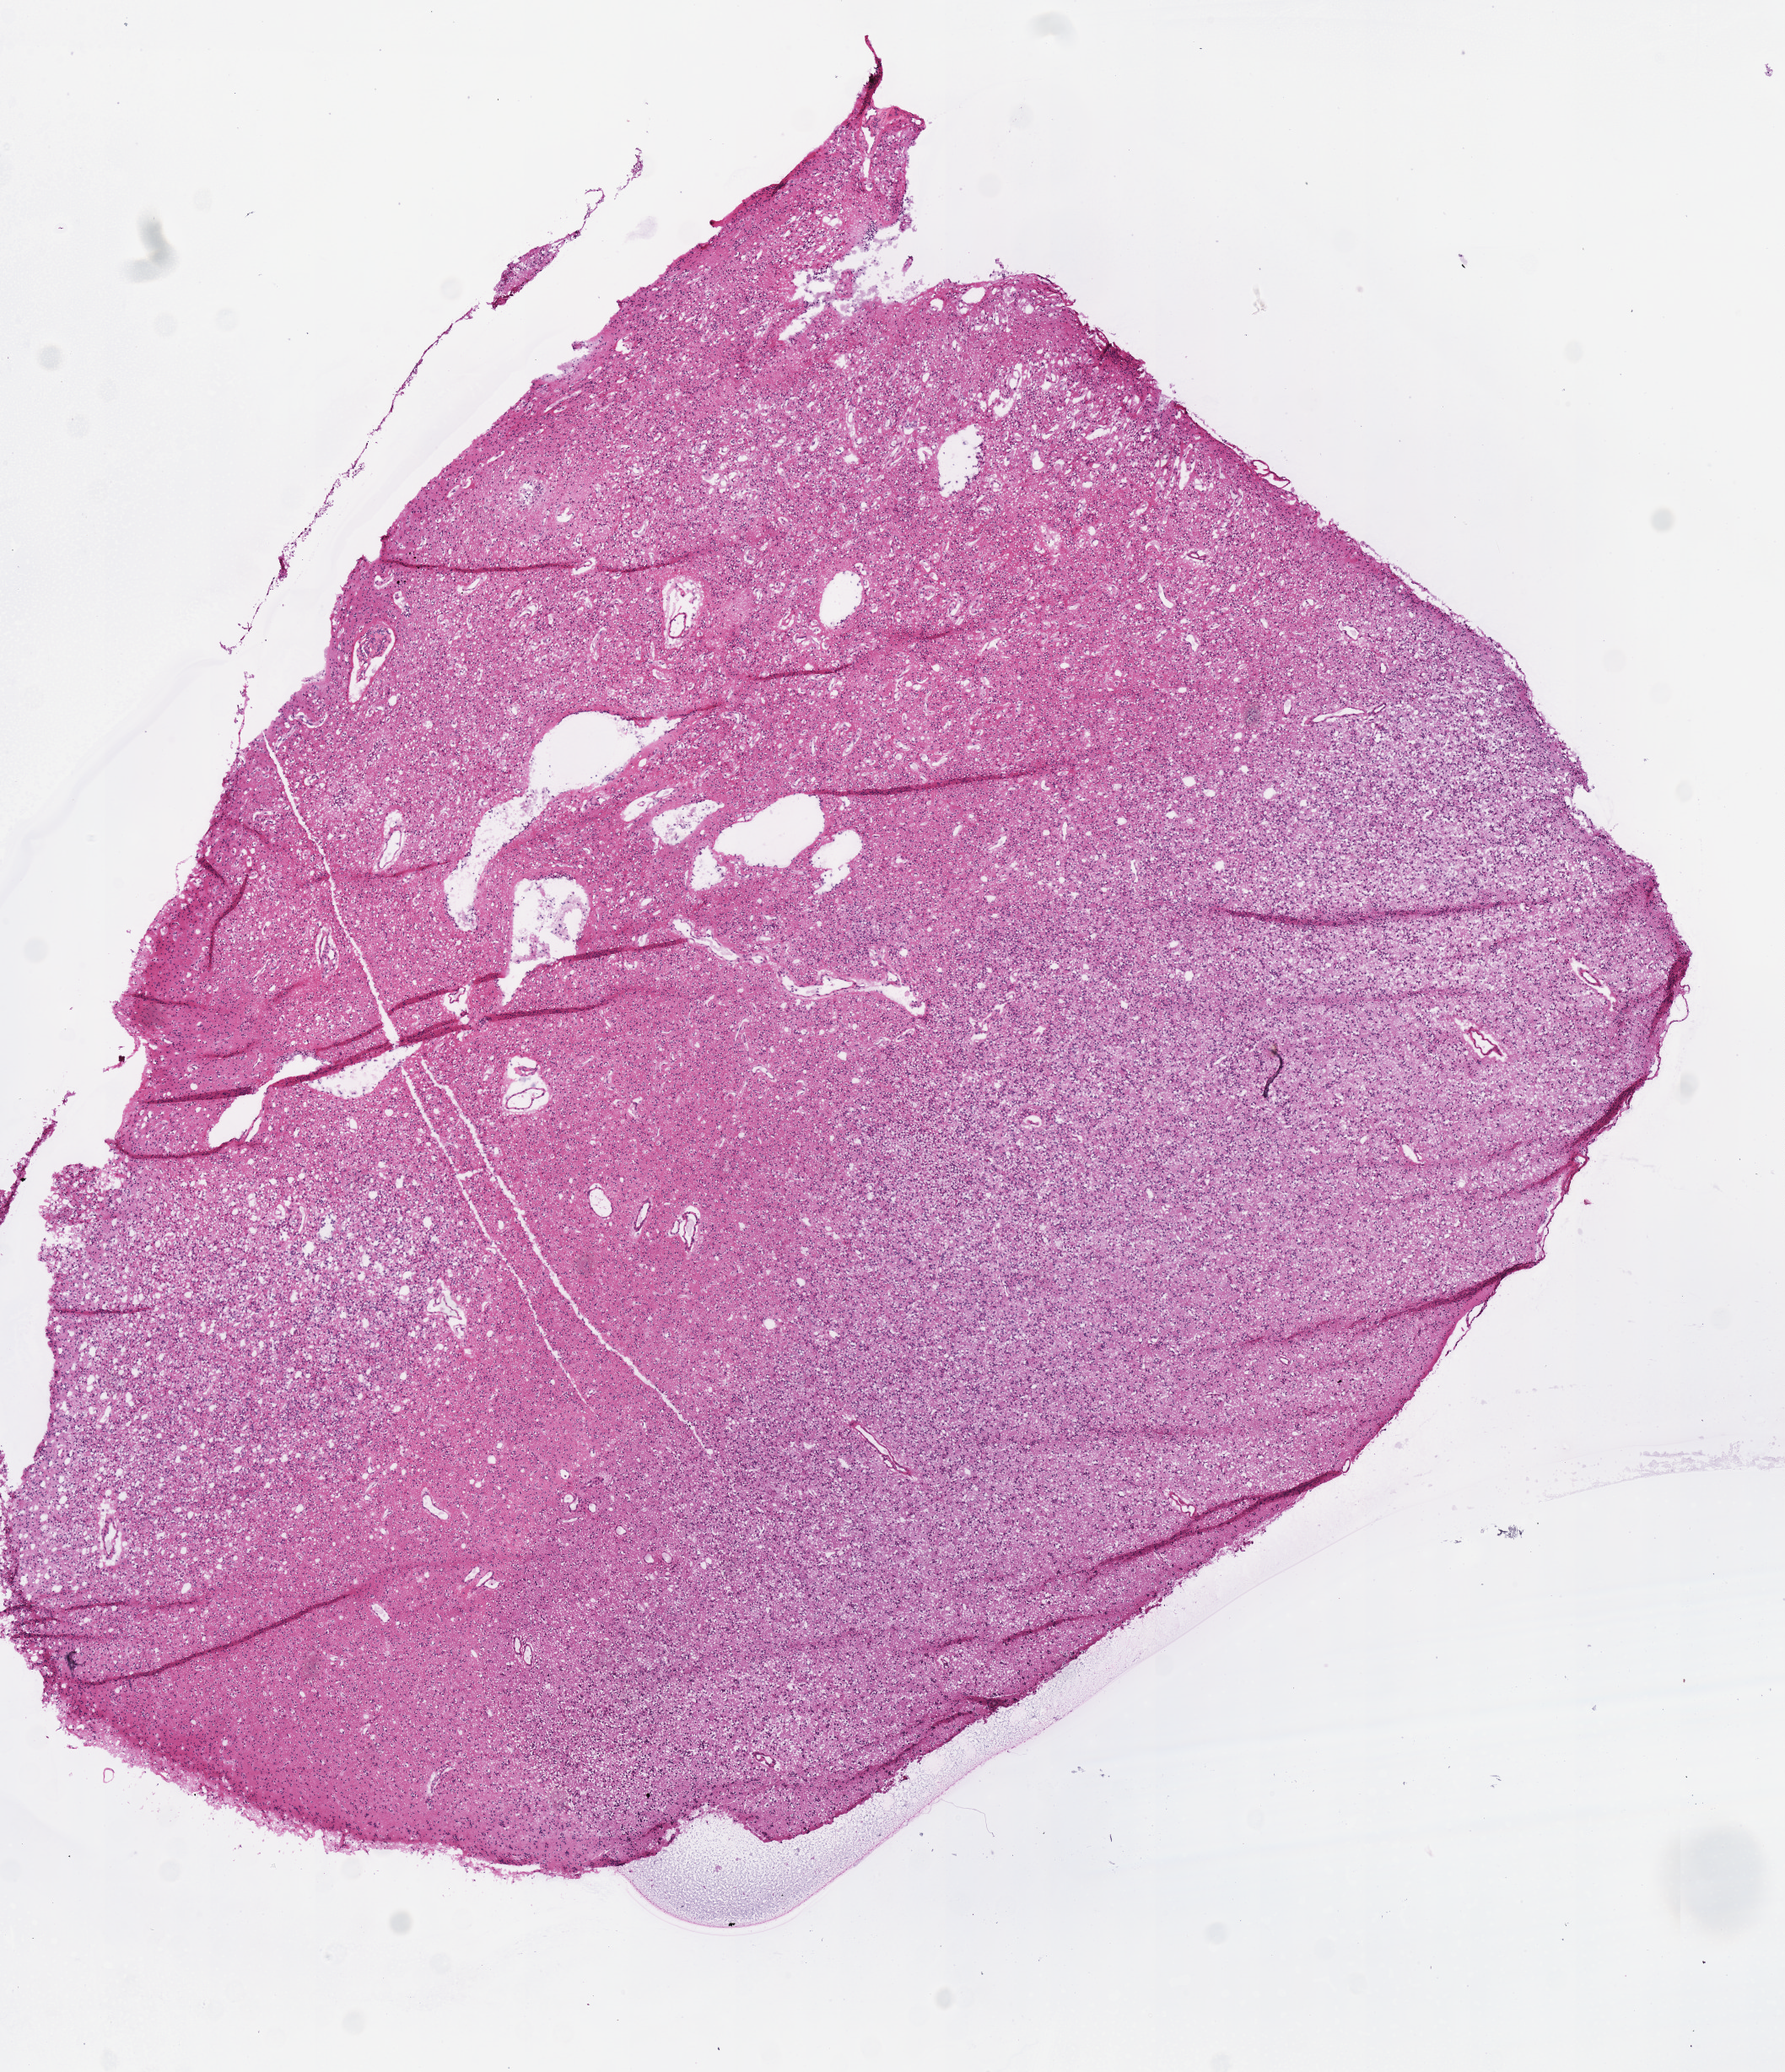
H&E-stained whole-slide image, whole scanned area (about 8.3 x 9.7 mm) shown as a low-resolution overview; frozen section from the top of the tissue portion; primary tumour sample from the brain. Female patient; age at initial diagnosis 31 years. Histologic grade: G3 (poorly differentiated). Pathologist review of this section (percent, as recorded): tumour cells 100%, tumour nuclei 75%, normal cells 0%, stromal cells 0%, necrosis 0%.
Laterality: left. Diagnosis: Oligodendroglioma, anaplastic (cerebrum).